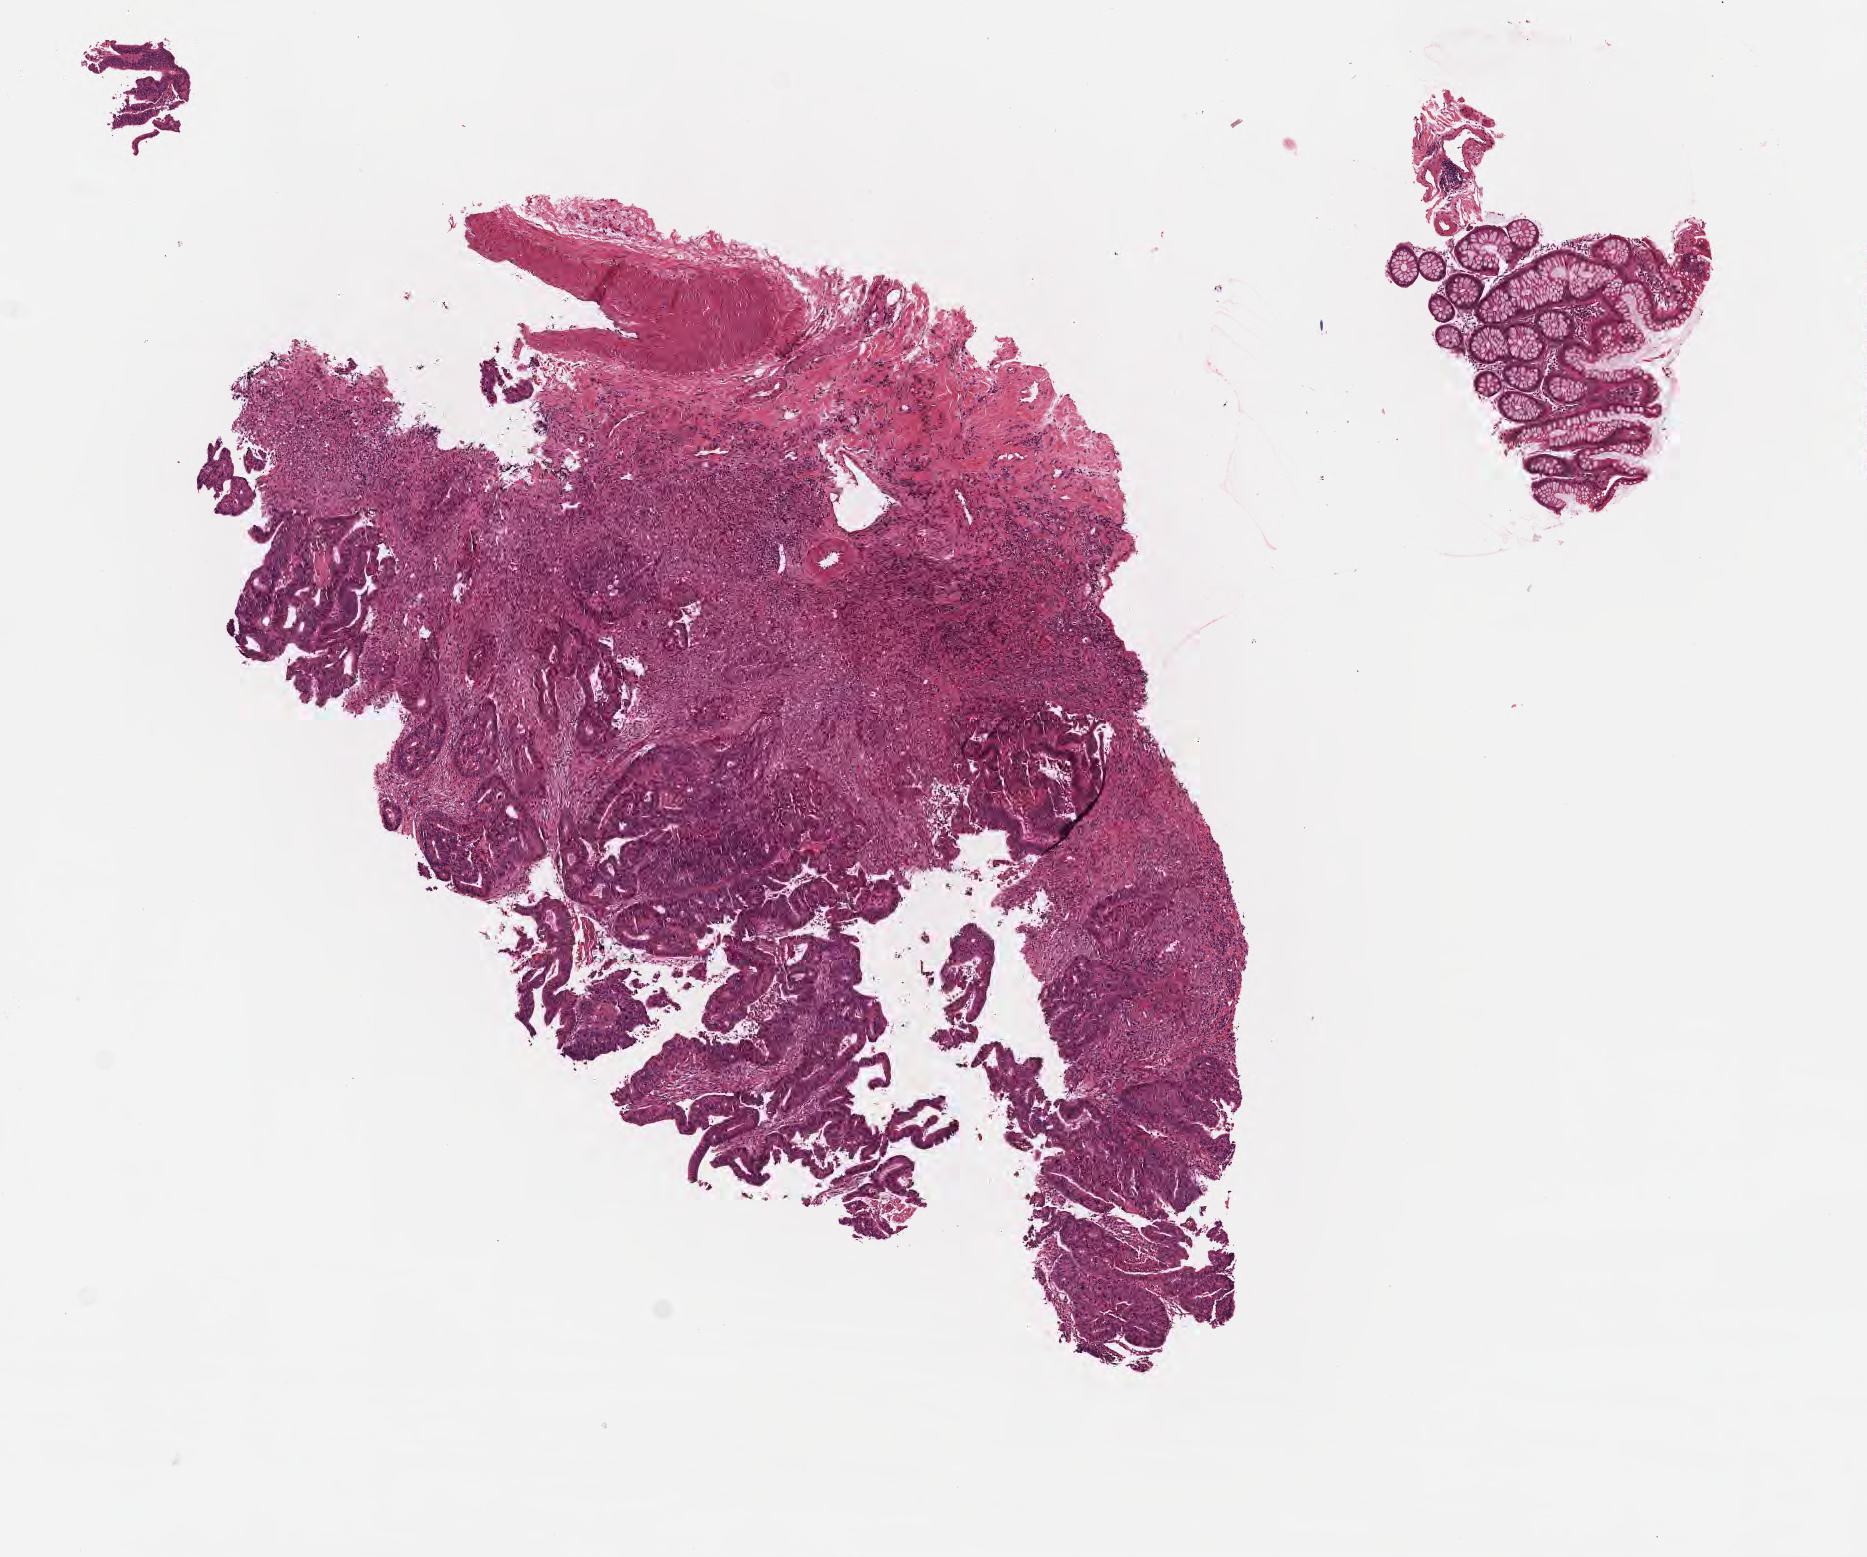
Digitized H&E-stained section — shown as a low-resolution overview of the whole scanned area (about 7.6 x 6.3 mm). FFPE section. Primary tumor. Site: ascending colon. Patient: female, age at initial diagnosis 83 years. Tumor grade: GB (borderline). Slide review estimates, as recorded: tumor cells 40%, tumor nuclei 50%, stromal cells 50%, necrosis 0%, normal cells 10%. Infiltration values recorded for this section: lymphocyte infiltration 0%, monocyte infiltration 0%, neutrophil infiltration 0%.
• AJCC pathologic stage: Stage IIA
• histologic diagnosis: Adenocarcinoma, NOS
• section: top of the tissue portion